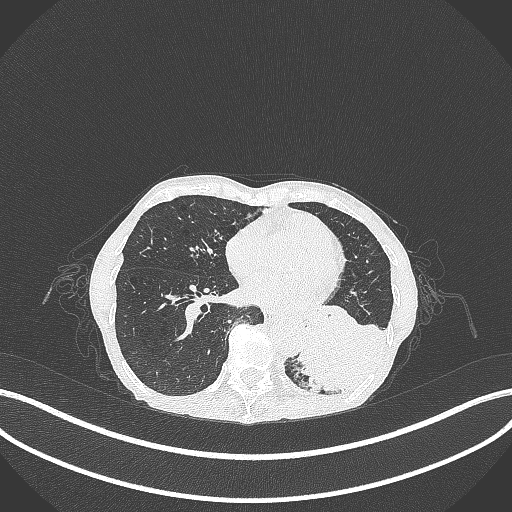
Chest CT, one axial slice; slice 98 of 347 in the series (ordered by position); 120 kVp; lung window (W 1500 / L -600 HU); 1 mm slice thickness; 512 × 512 image matrix, field of view 400 × 400 mm. Patient: female, 70 years. Case-level facts recorded for this patient, not image findings: clinical TNM (as recorded): T3 N0 M0.
Structures marked on this image (bounding box drawn by a radiologist):
- lung tumour (recorded histology: small cell carcinoma): box from (x=298, y=316) to (x=405, y=393) px